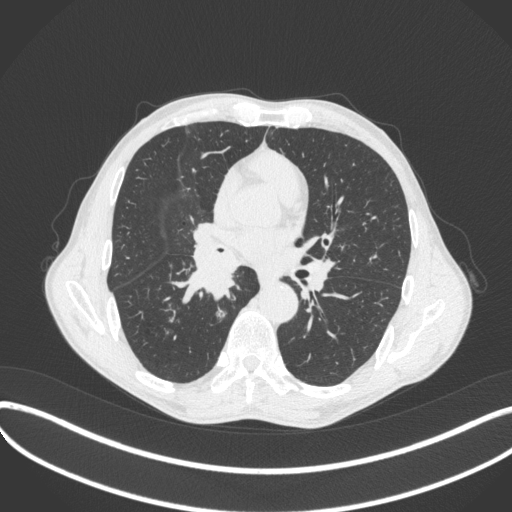
Chest CT, one axial slice. Slice 226 of 481 in the series (ordered by position). 120 kVp. Lung window (W 1500 / L -600 HU). 1 mm slice thickness. 512 × 512 image matrix, field of view 400 × 400 mm. Patient: male, 65 years. From the clinical record (not read from this slice): clinical TNM (as recorded): T2a N0 M0; histopathological grade: G2.
Structures marked on this image (bounding box drawn by a radiologist):
- lung tumour (recorded histology: squamous cell carcinoma): bounding box <183,227,246,313> (left, top, right, bottom; pixels)